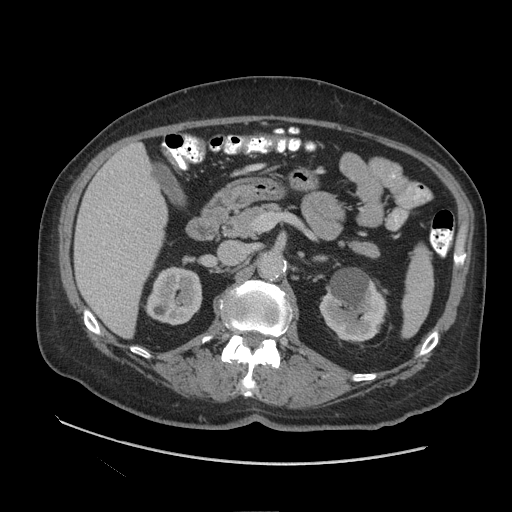
Contrast-enhanced abdominal CT (liver protocol), one axial slice; position 44 of 109 along the scan axis; reconstruction kernel STANDARD; soft-tissue window (W 400 / L 40 HU); 2.5 mm slice thickness; 512 × 512 image matrix, field of view 420 × 420 mm. From the clinical record (not read from this slice): diagnosis: hepatocellular carcinoma (patient treated with transarterial chemoembolisation; whether this scan precedes or follows treatment is not stated here); TNM stage (as recorded): Stage-I.
Outlined on this slice (semi-automatically segmented with operator editing):
- liver parenchyma outside the tumour (the mass and vessels are separate outlines, so this box may not span the whole liver): box from (x=74, y=144) to (x=168, y=336) px
- liver vessels: (x=89, y=171)–(x=143, y=293)